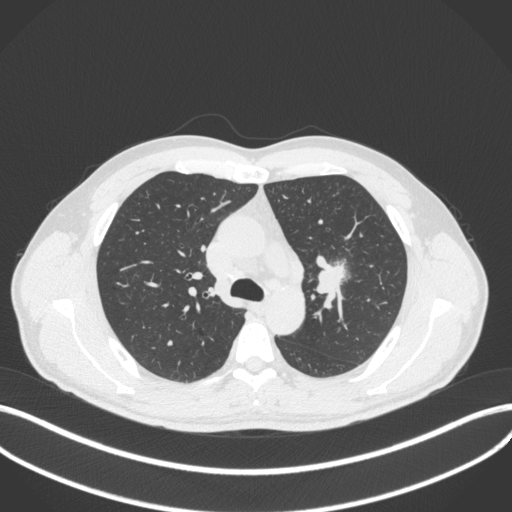
Chest CT, one axial slice; slice 288 of 383 in the series (ordered by position); reconstruction kernel B31f; 120 kVp; lung window (W 1500 / L -600 HU); 1 mm slice thickness; 512 × 512 image matrix, field of view 400 × 400 mm. Patient: male, 50 years. Case-level facts recorded for this patient, not image findings: clinical TNM (as recorded): T1c N1 M1b.
Structures marked on this image (rectangle marked by the reading radiologist):
- lung tumour (recorded histology: squamous cell carcinoma): bounding box [x1, y1, x2, y2] px = [309, 255, 350, 299]